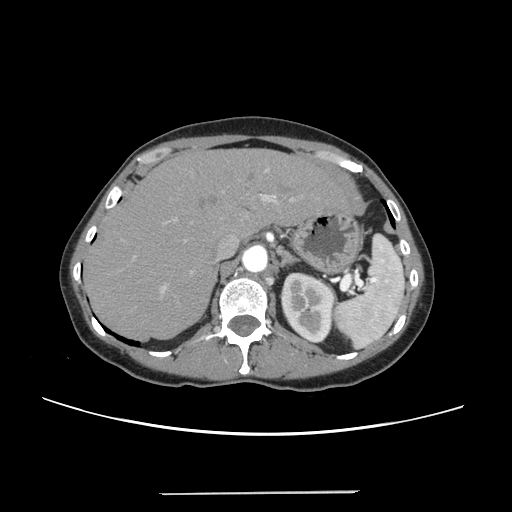
Contrast-enhanced abdominal CT, one axial slice. Slice 177 of 240 in the series (ordered by position). 120 kVp. Intravenous contrast given. Soft-tissue window (W 400 / L 40 HU). 1.25 mm slice thickness. 512 × 512 image matrix, field of view 371 × 371 mm. Female patient, age 60 years. Case-level facts recorded for this patient, not image findings: diagnosis: colorectal cancer liver metastases, imaged before liver resection; multiple liver metastases: no; largest metastasis: 1.5 cm; disease in both lobes: no.
Annotated regions visible in this slice (outlined manually by an expert reader):
- liver: bounding box <86,150,349,339> (left, top, right, bottom; pixels)
- planned liver remnant (the part of the liver to remain after resection): <86,150,348,339>
- portal vein (with intrahepatic branches): <133,170,296,295>